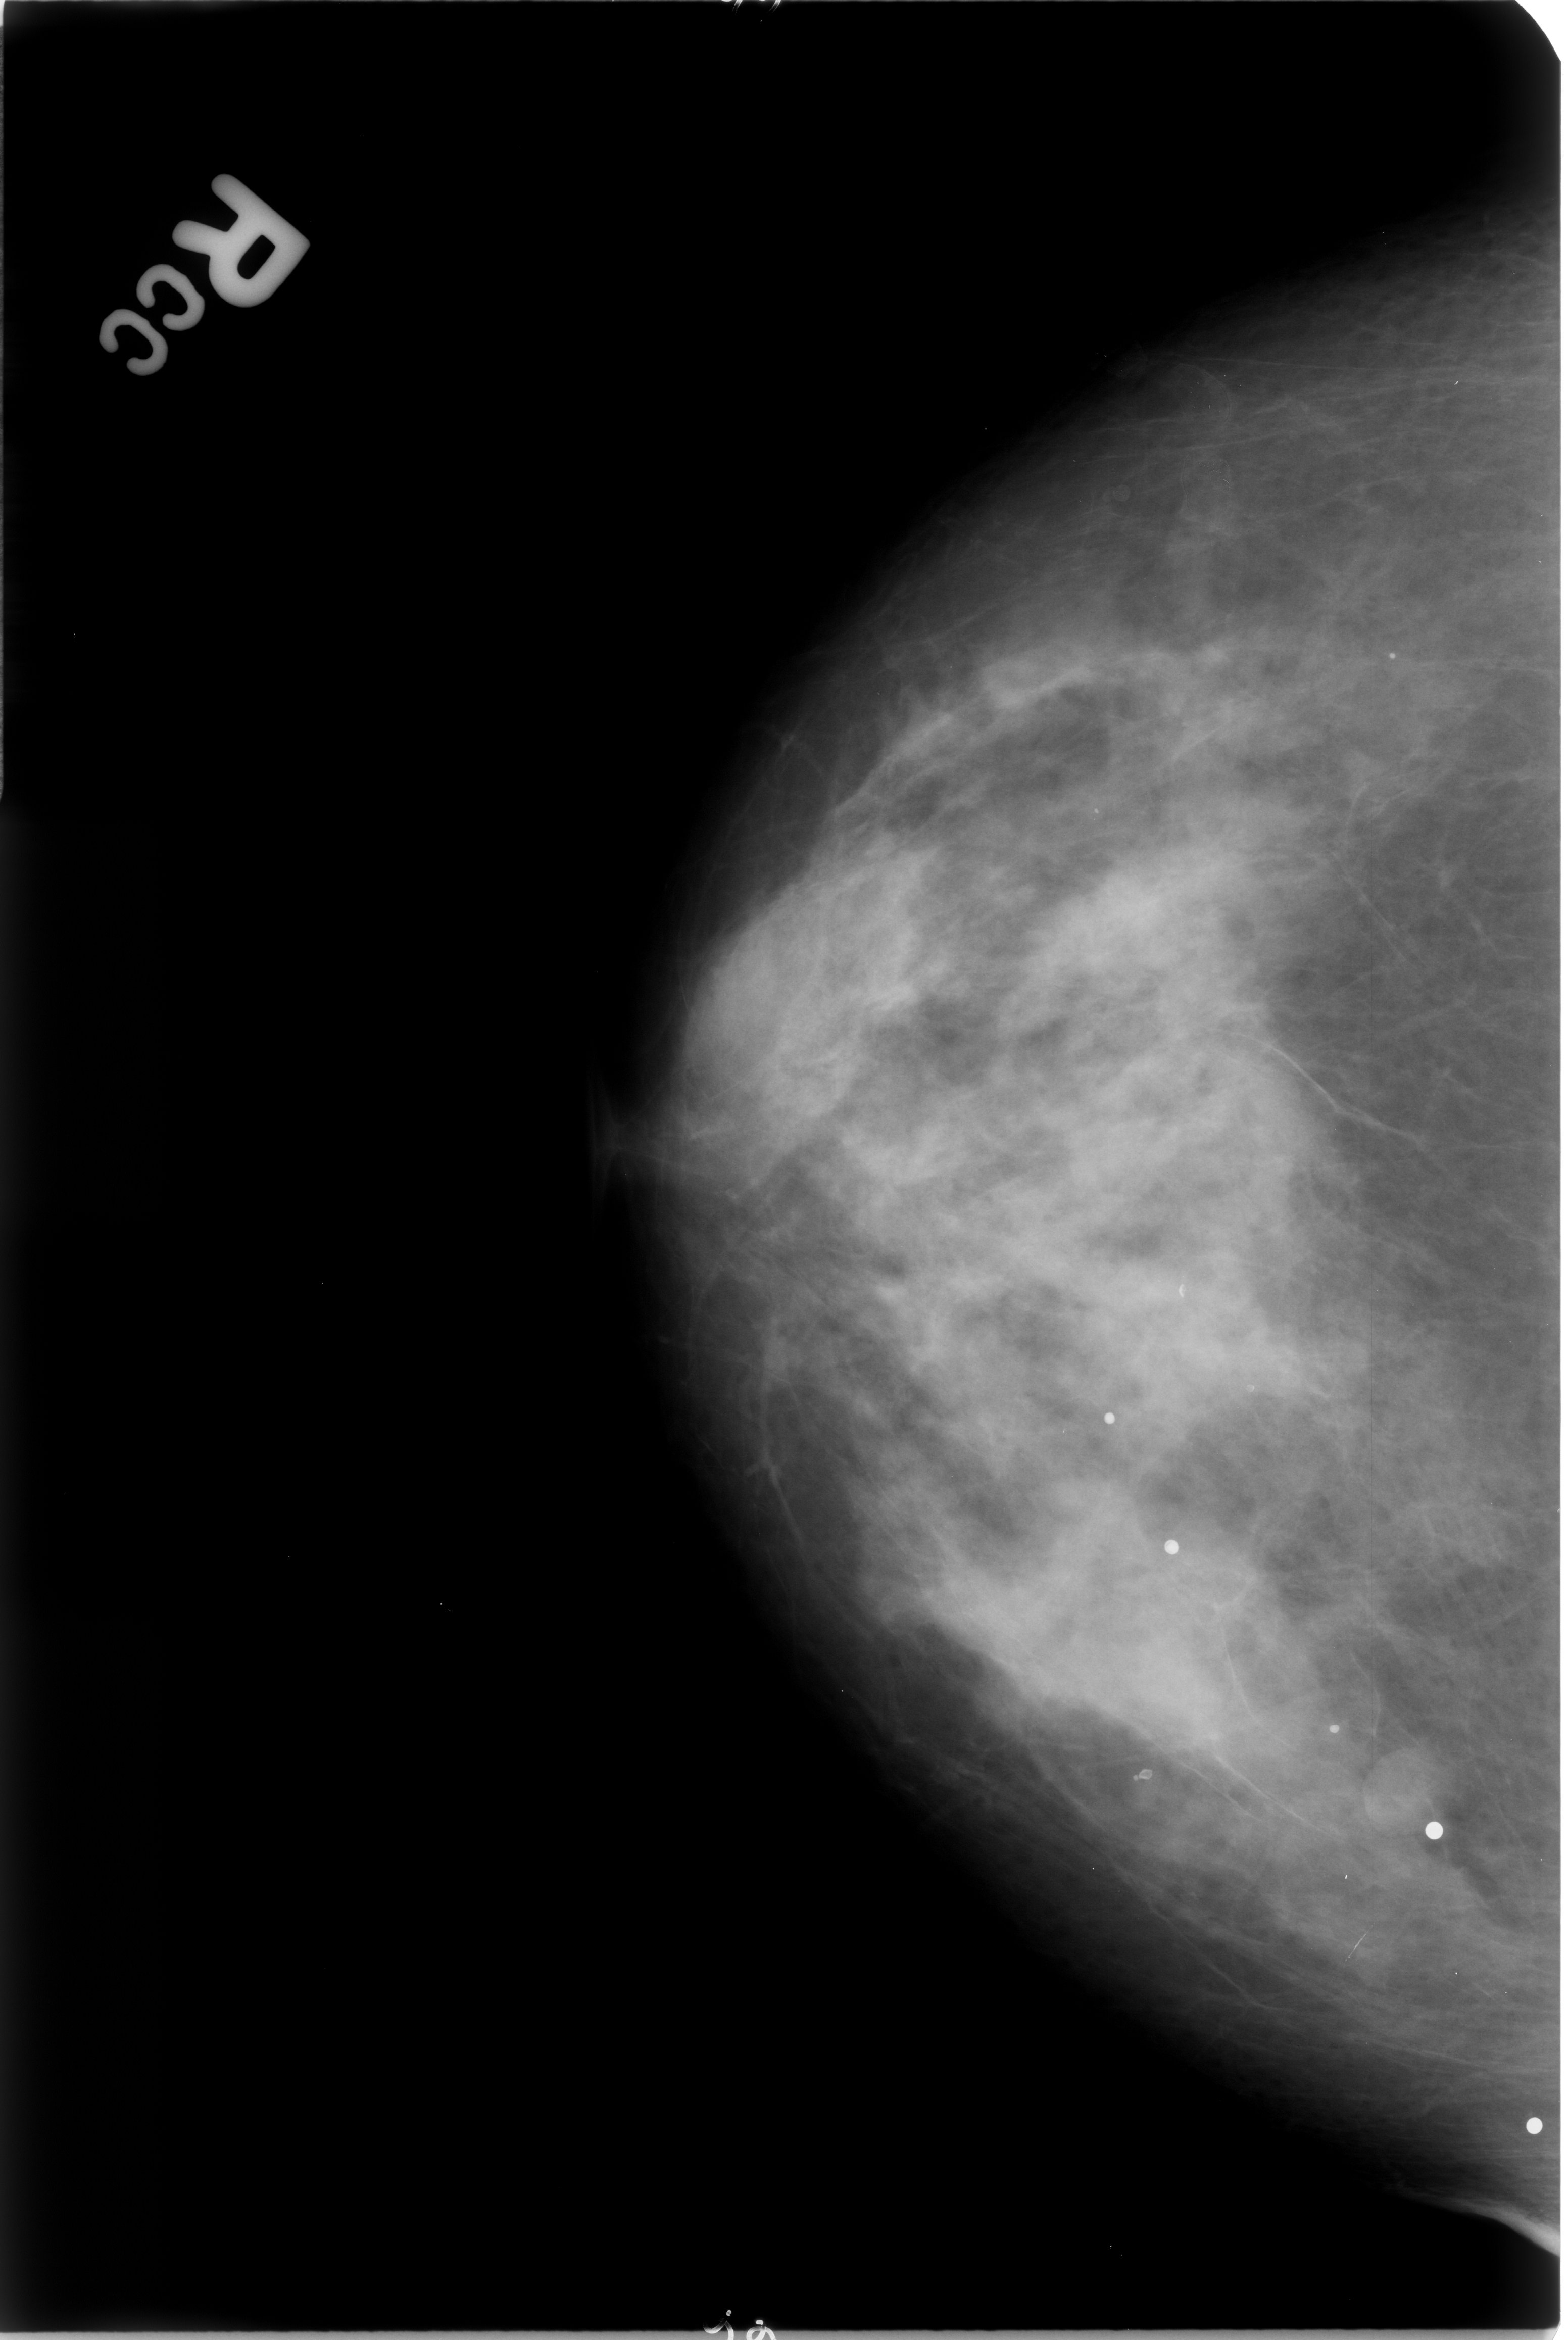
Digitized screen-film mammogram. Right breast. CC view. 1568 × 2340 image matrix.
Marked abnormalities (boxes around the expert regions of interest):
- Finding 1 of 5: calcifications, morphology round and regular / lucent center; BI-RADS assessment category 2; subtlety rating 5 on a 1 (subtle) to 5 (obvious) scale; outcome (as recorded, no biopsy): benign without callback (not worked up further): box from (x=1095, y=1406) to (x=1120, y=1432) px
- Finding 2 of 5: calcifications, morphology round and regular / lucent center; BI-RADS assessment category 2; benign; no additional work-up was recommended (outcome (as recorded, no biopsy): benign without callback): (x=1127, y=1753)–(x=1165, y=1820)
- Finding 3 of 5: calcifications, morphology round and regular / lucent center; BI-RADS assessment category 2; subtlety rating 5 on a 1 (subtle) to 5 (obvious) scale; benign; no additional work-up was recommended (outcome (as recorded, no biopsy): benign without callback): (x=1163, y=1531)–(x=1185, y=1557)
- Finding 4 of 5: calcifications, morphology round and regular / lucent center; BI-RADS assessment category 2; subtlety rating 5 on a 1 (subtle) to 5 (obvious) scale; outcome (as recorded, no biopsy): benign without callback (not worked up further): (x=1313, y=1713)–(x=1347, y=1743)
- Finding 5 of 5: calcifications, morphology round and regular / lucent center; BI-RADS assessment category 2; subtlety rating 5 on a 1 (subtle) to 5 (obvious) scale; benign; no additional work-up was recommended (outcome (as recorded, no biopsy): benign without callback): (x=1378, y=638)–(x=1411, y=676)